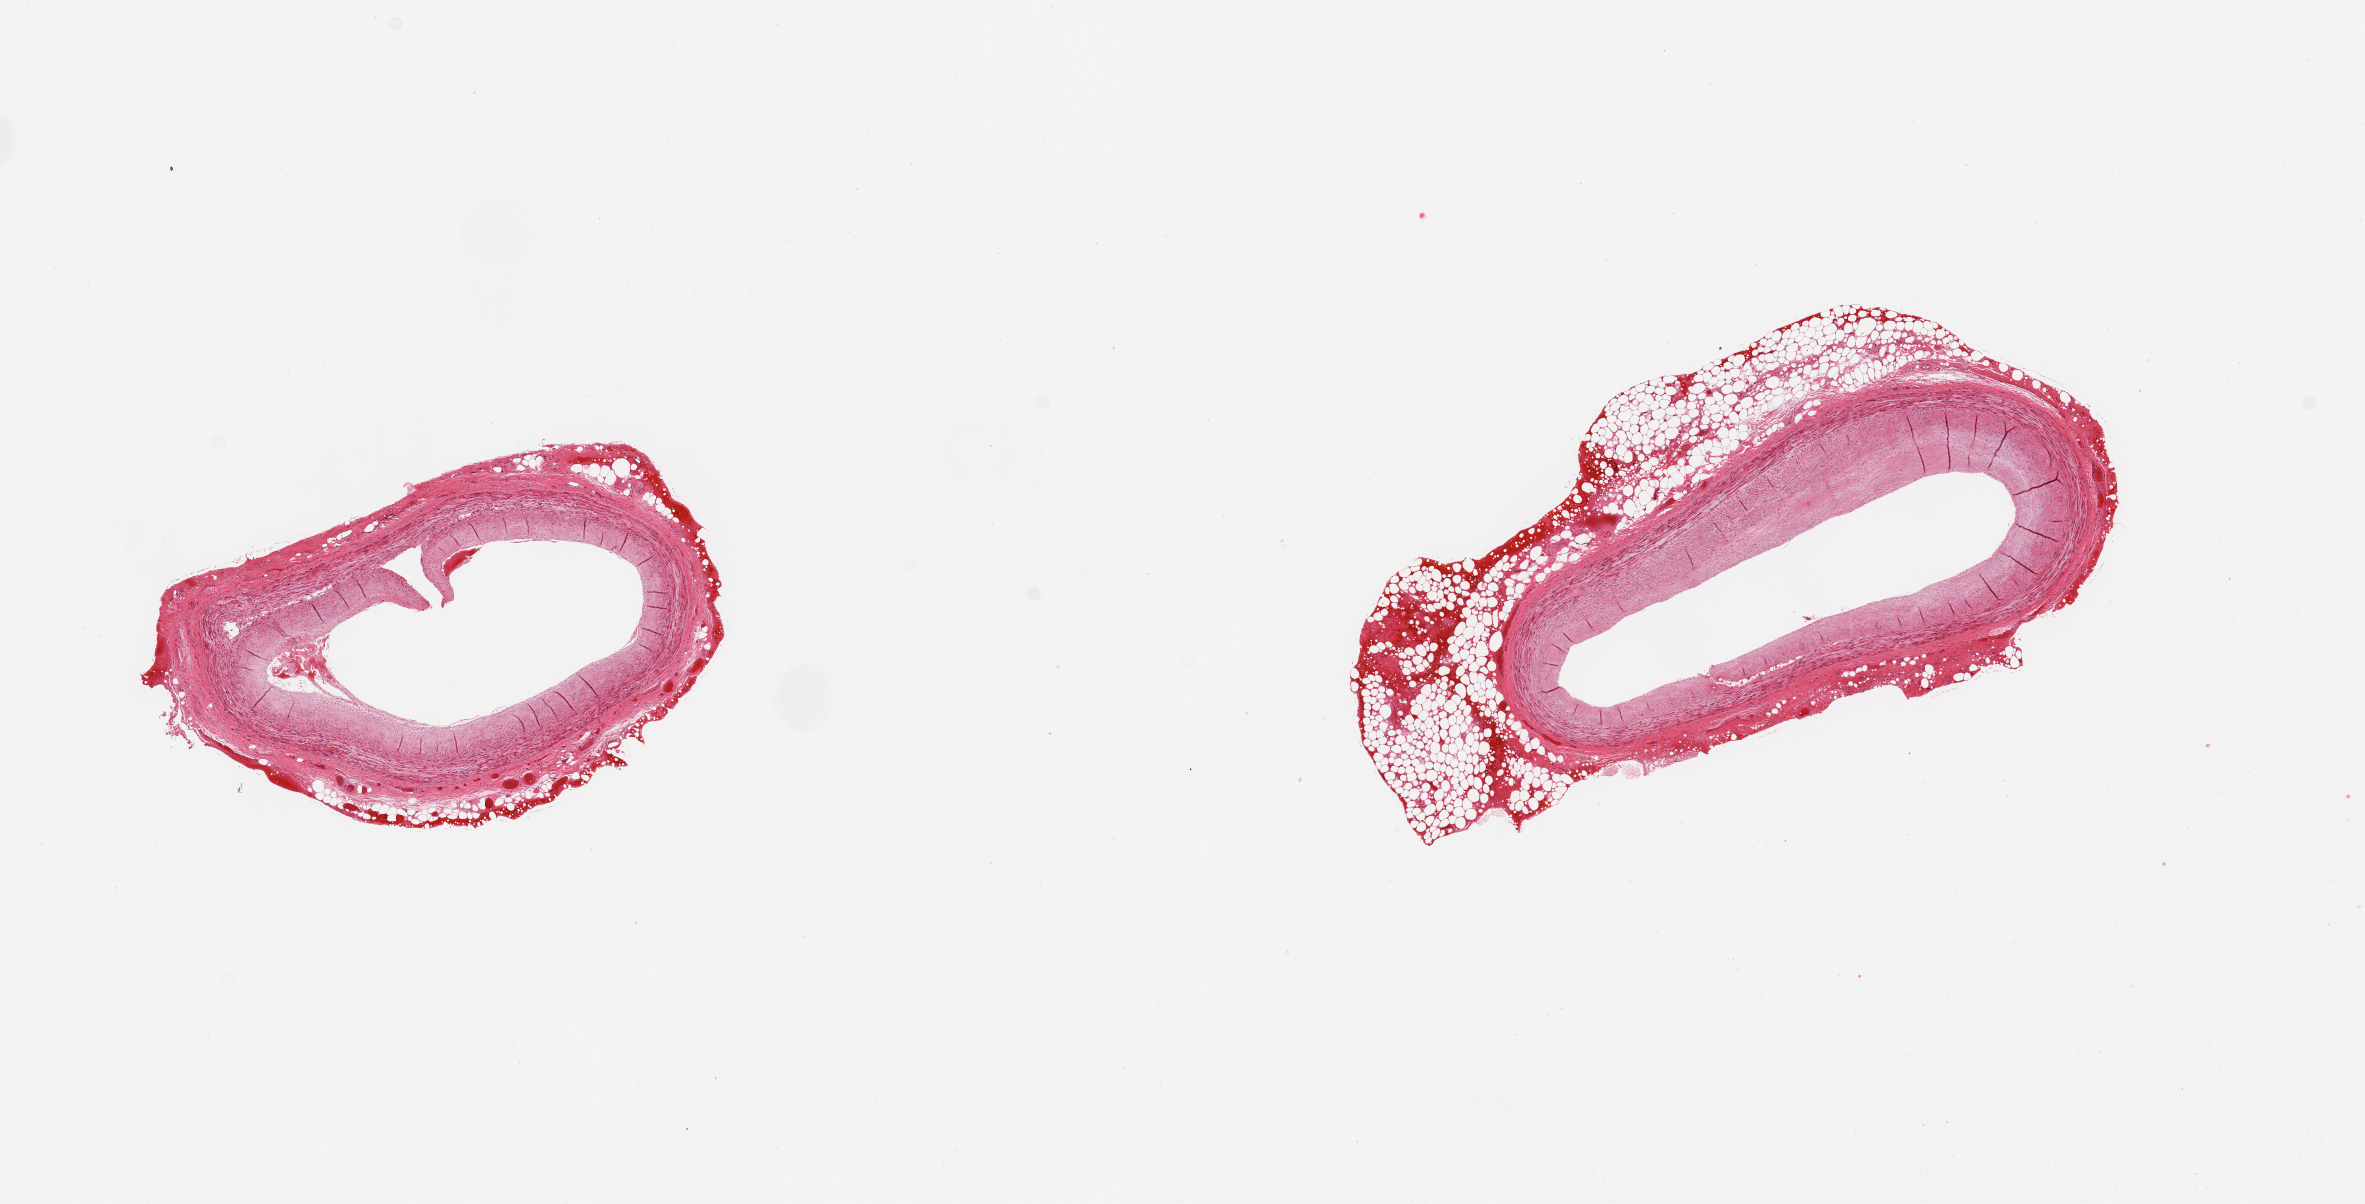
Whole-slide image, haematoxylin and eosin stain, shown as a low-resolution overview of the whole scanned area (about 18.7 x 9.5 mm); PAXgene-fixed, paraffin-embedded tissue; target tissue: coronary artery; donor tissue sample. Male donor.
* review note (as recorded): 2 pieces, partial rim of fat up to ~1mm; Minimal atherosis